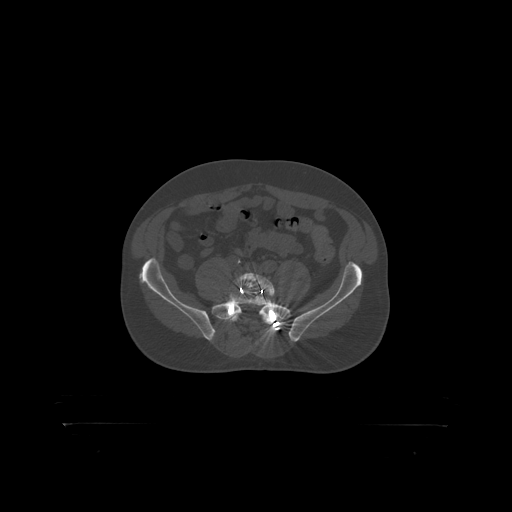
CT including the spine, one axial slice; 120 kVp; bone window (W 1800 / L 400 HU); 1.25 mm slice thickness; 512 × 512 image matrix. Male patient, age 46 years. Case-level facts recorded for this patient, not image findings: primary cancer: skin.
Annotated regions visible in this slice (semi-automatic segmentation, software-assisted and operator-edited):
- L5 vertebra: bounding box <235,274,275,297> (left, top, right, bottom; pixels)